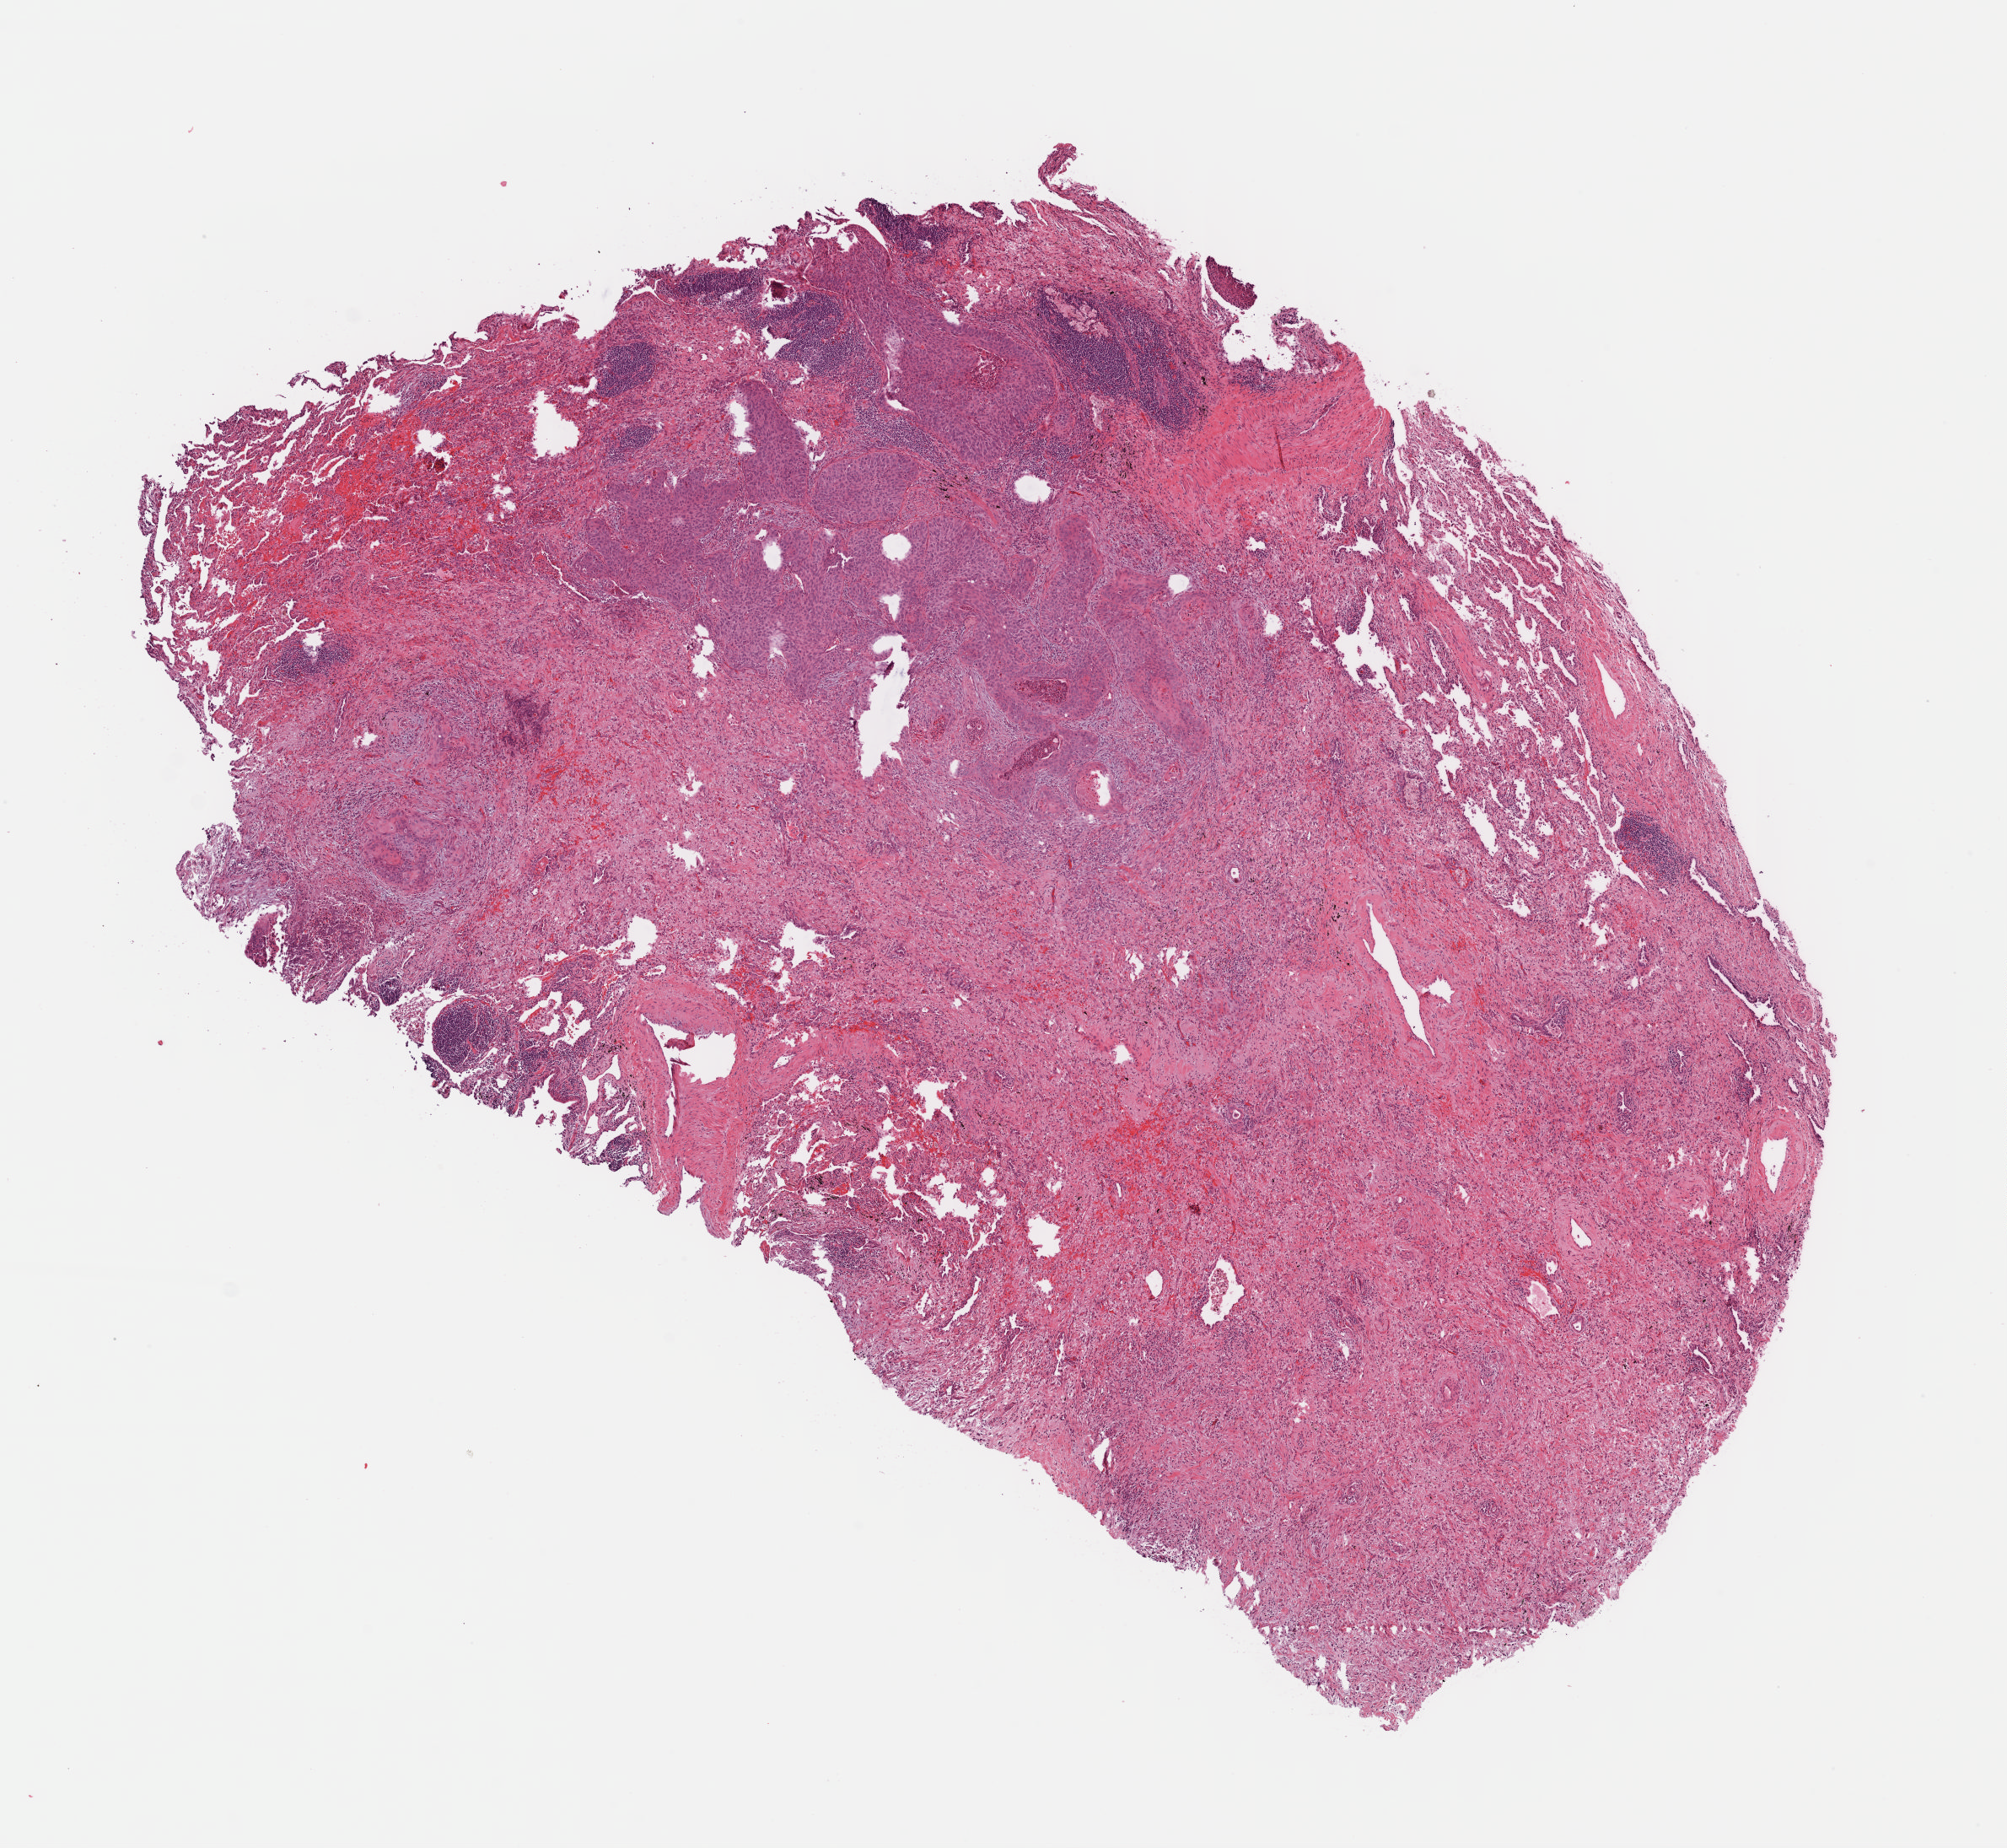
Whole-slide histology image, H&E, shown as a low-resolution overview of the whole scanned area (about 9.4 x 8.6 mm, slide scanned at 40x), formalin-fixed paraffin-embedded (FFPE) diagnostic section, primary tumour sample from the lung. Male patient; age at initial diagnosis 68 years.
AJCC pathologic stage: IIB. Diagnosis: Squamous cell carcinoma, keratinizing, NOS (upper lobe, lung). Laterality: right.